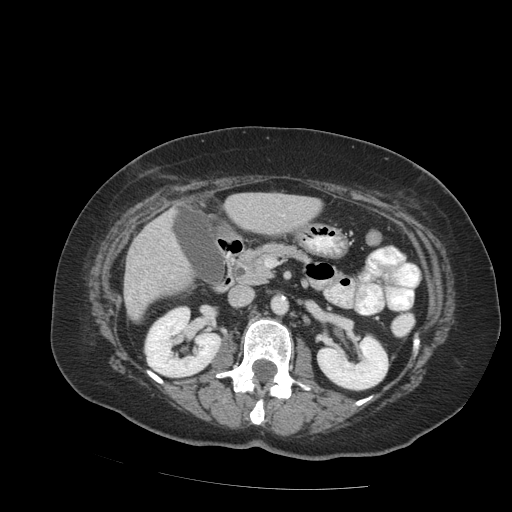
Contrast-enhanced abdominal CT (liver protocol), one axial slice. Position 34 of 99 along the scan axis. 140 kVp. Soft-tissue window (W 400 / L 40 HU). 512 × 512 image matrix, field of view 400 × 400 mm. Case-level facts recorded for this patient, not image findings: diagnosis: hepatocellular carcinoma (patient treated with transarterial chemoembolisation; whether this scan precedes or follows treatment is not stated here); TNM stage (as recorded): Stage-IVB; Child-Pugh class: A.
Annotated regions visible in this slice (semi-automatic segmentation, software-assisted and operator-edited):
- liver parenchyma outside the tumour (the mass and vessels are separate outlines, so this box may not span the whole liver): bounding box [x1, y1, x2, y2] px = [124, 192, 312, 320]
- liver vessels: [128, 283, 144, 299]